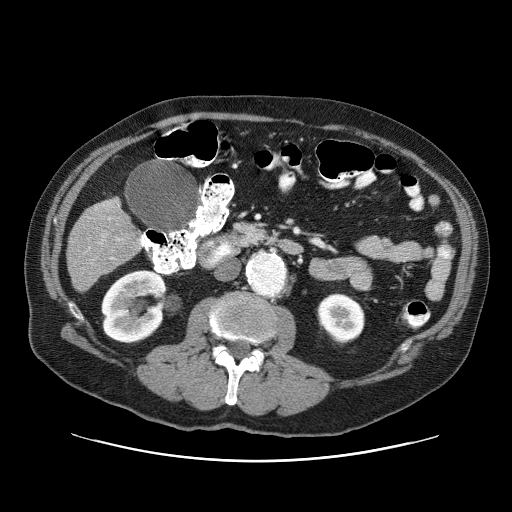
Contrast-enhanced abdominal CT (liver protocol), one axial slice. Slice 13 of 87 in the series (ordered by position). One of 3 acquisitions stored at this slice position. Soft-tissue window (W 400 / L 40 HU). 512 × 512 image matrix. From the clinical record (not read from this slice): diagnosis: hepatocellular carcinoma (patient treated with transarterial chemoembolisation; whether this scan precedes or follows treatment is not stated here); TNM stage (as recorded): Stage-IIIA; Child-Pugh class: A; tumour differentiation: well differentiated; tumour nodularity: multinodular.
Annotated regions visible in this slice (semi-automatically segmented with operator editing):
- liver parenchyma outside the tumour (the mass and vessels are separate outlines, so this box may not span the whole liver): bounding box <66,198,136,292> (left, top, right, bottom; pixels)
- liver vessels: <108,217,114,259>